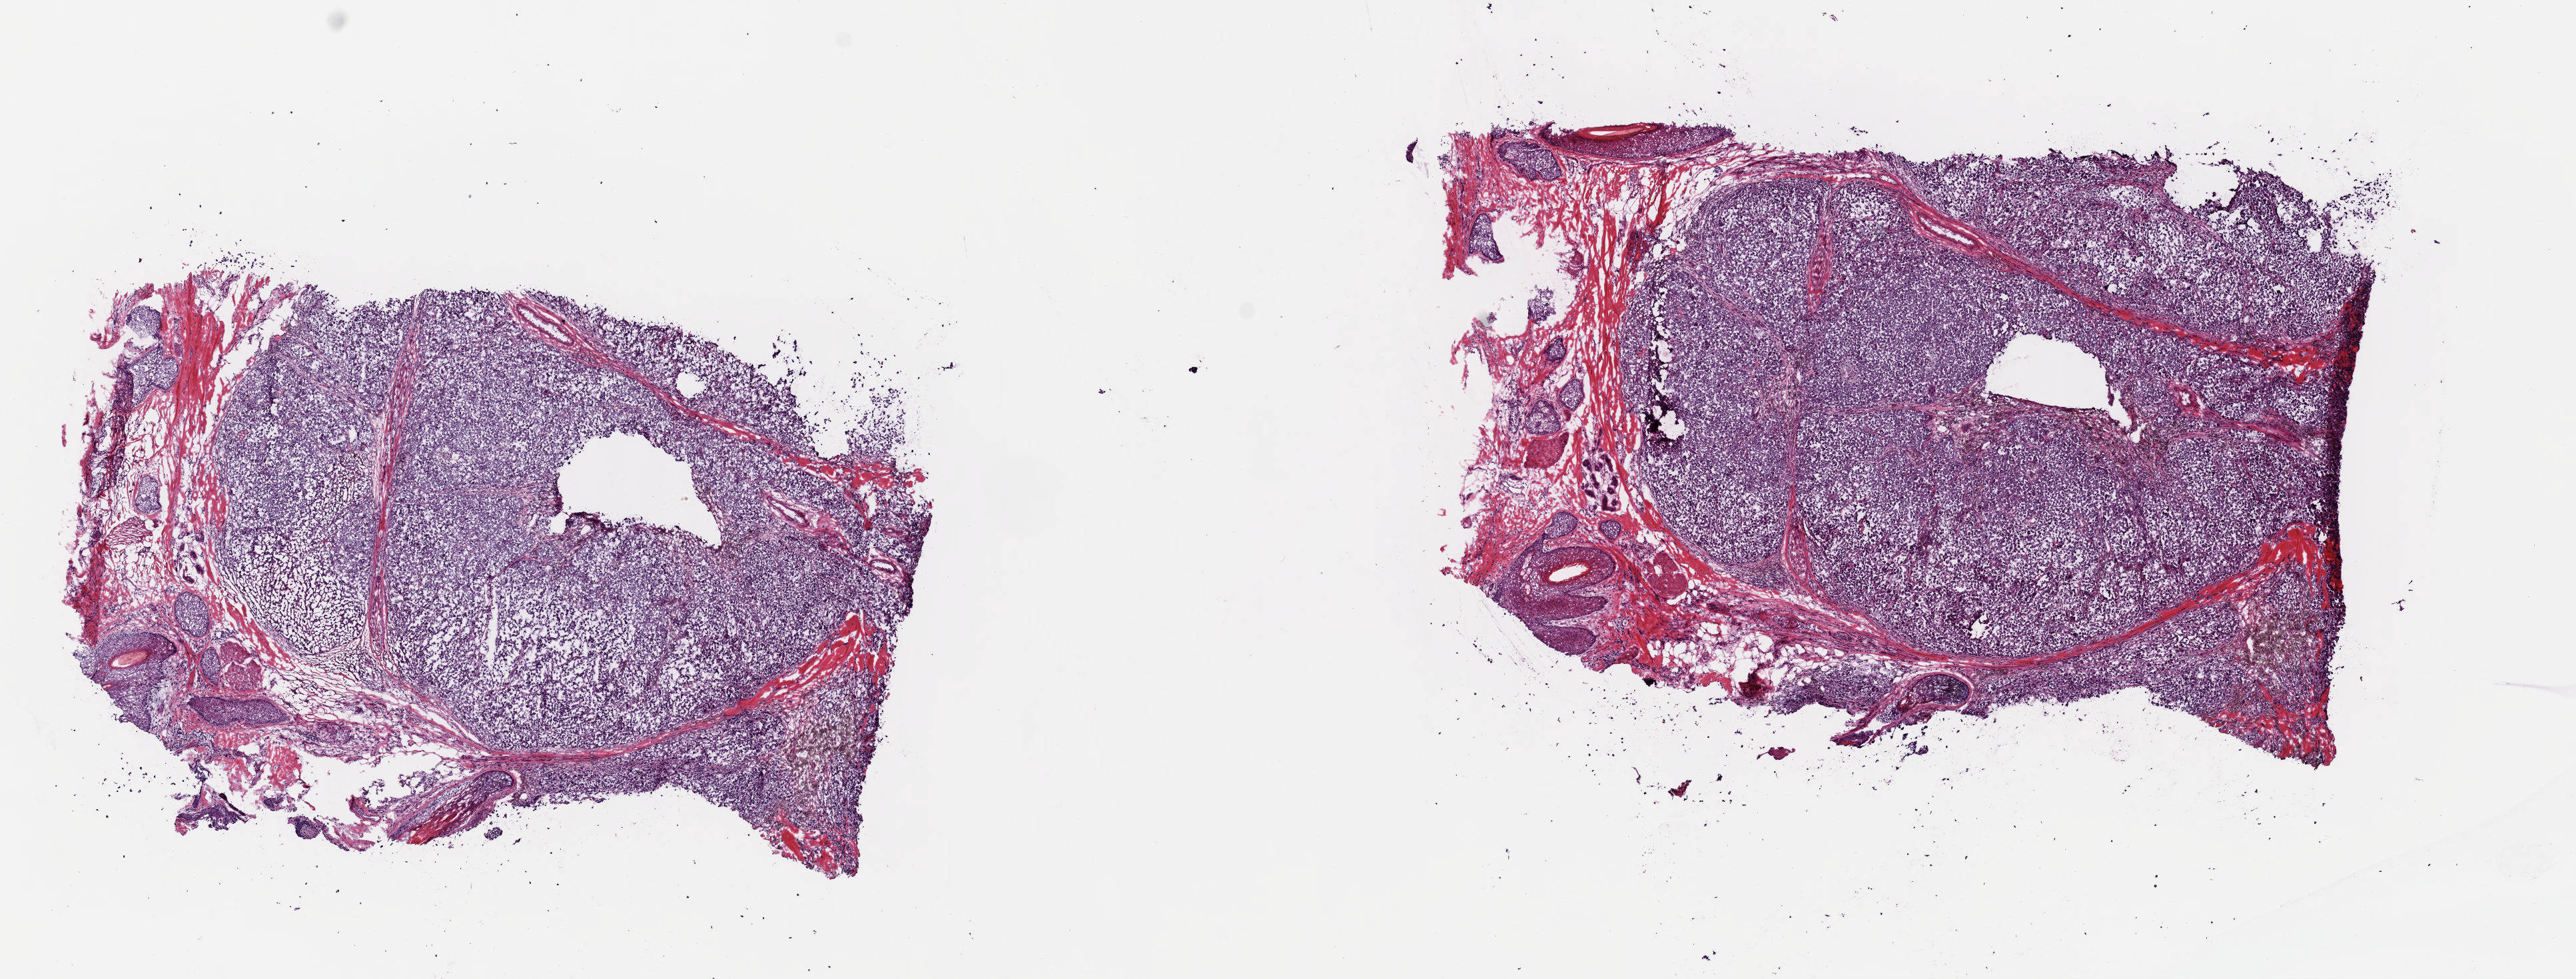
Digitized Hematoxylin and eosin (H&E) stained tissue section (whole slide), a low-resolution overview of the entire scanned area, about 15.3 x 5.8 mm (acquisition: 40x scan), frozen section from the top of the tissue portion, metastatic tumour sample, sampled site not recorded. Male, age 53 years at initial diagnosis.
This section: metastatic tumour tissue. Patient diagnosis: Malignant melanoma, NOS.